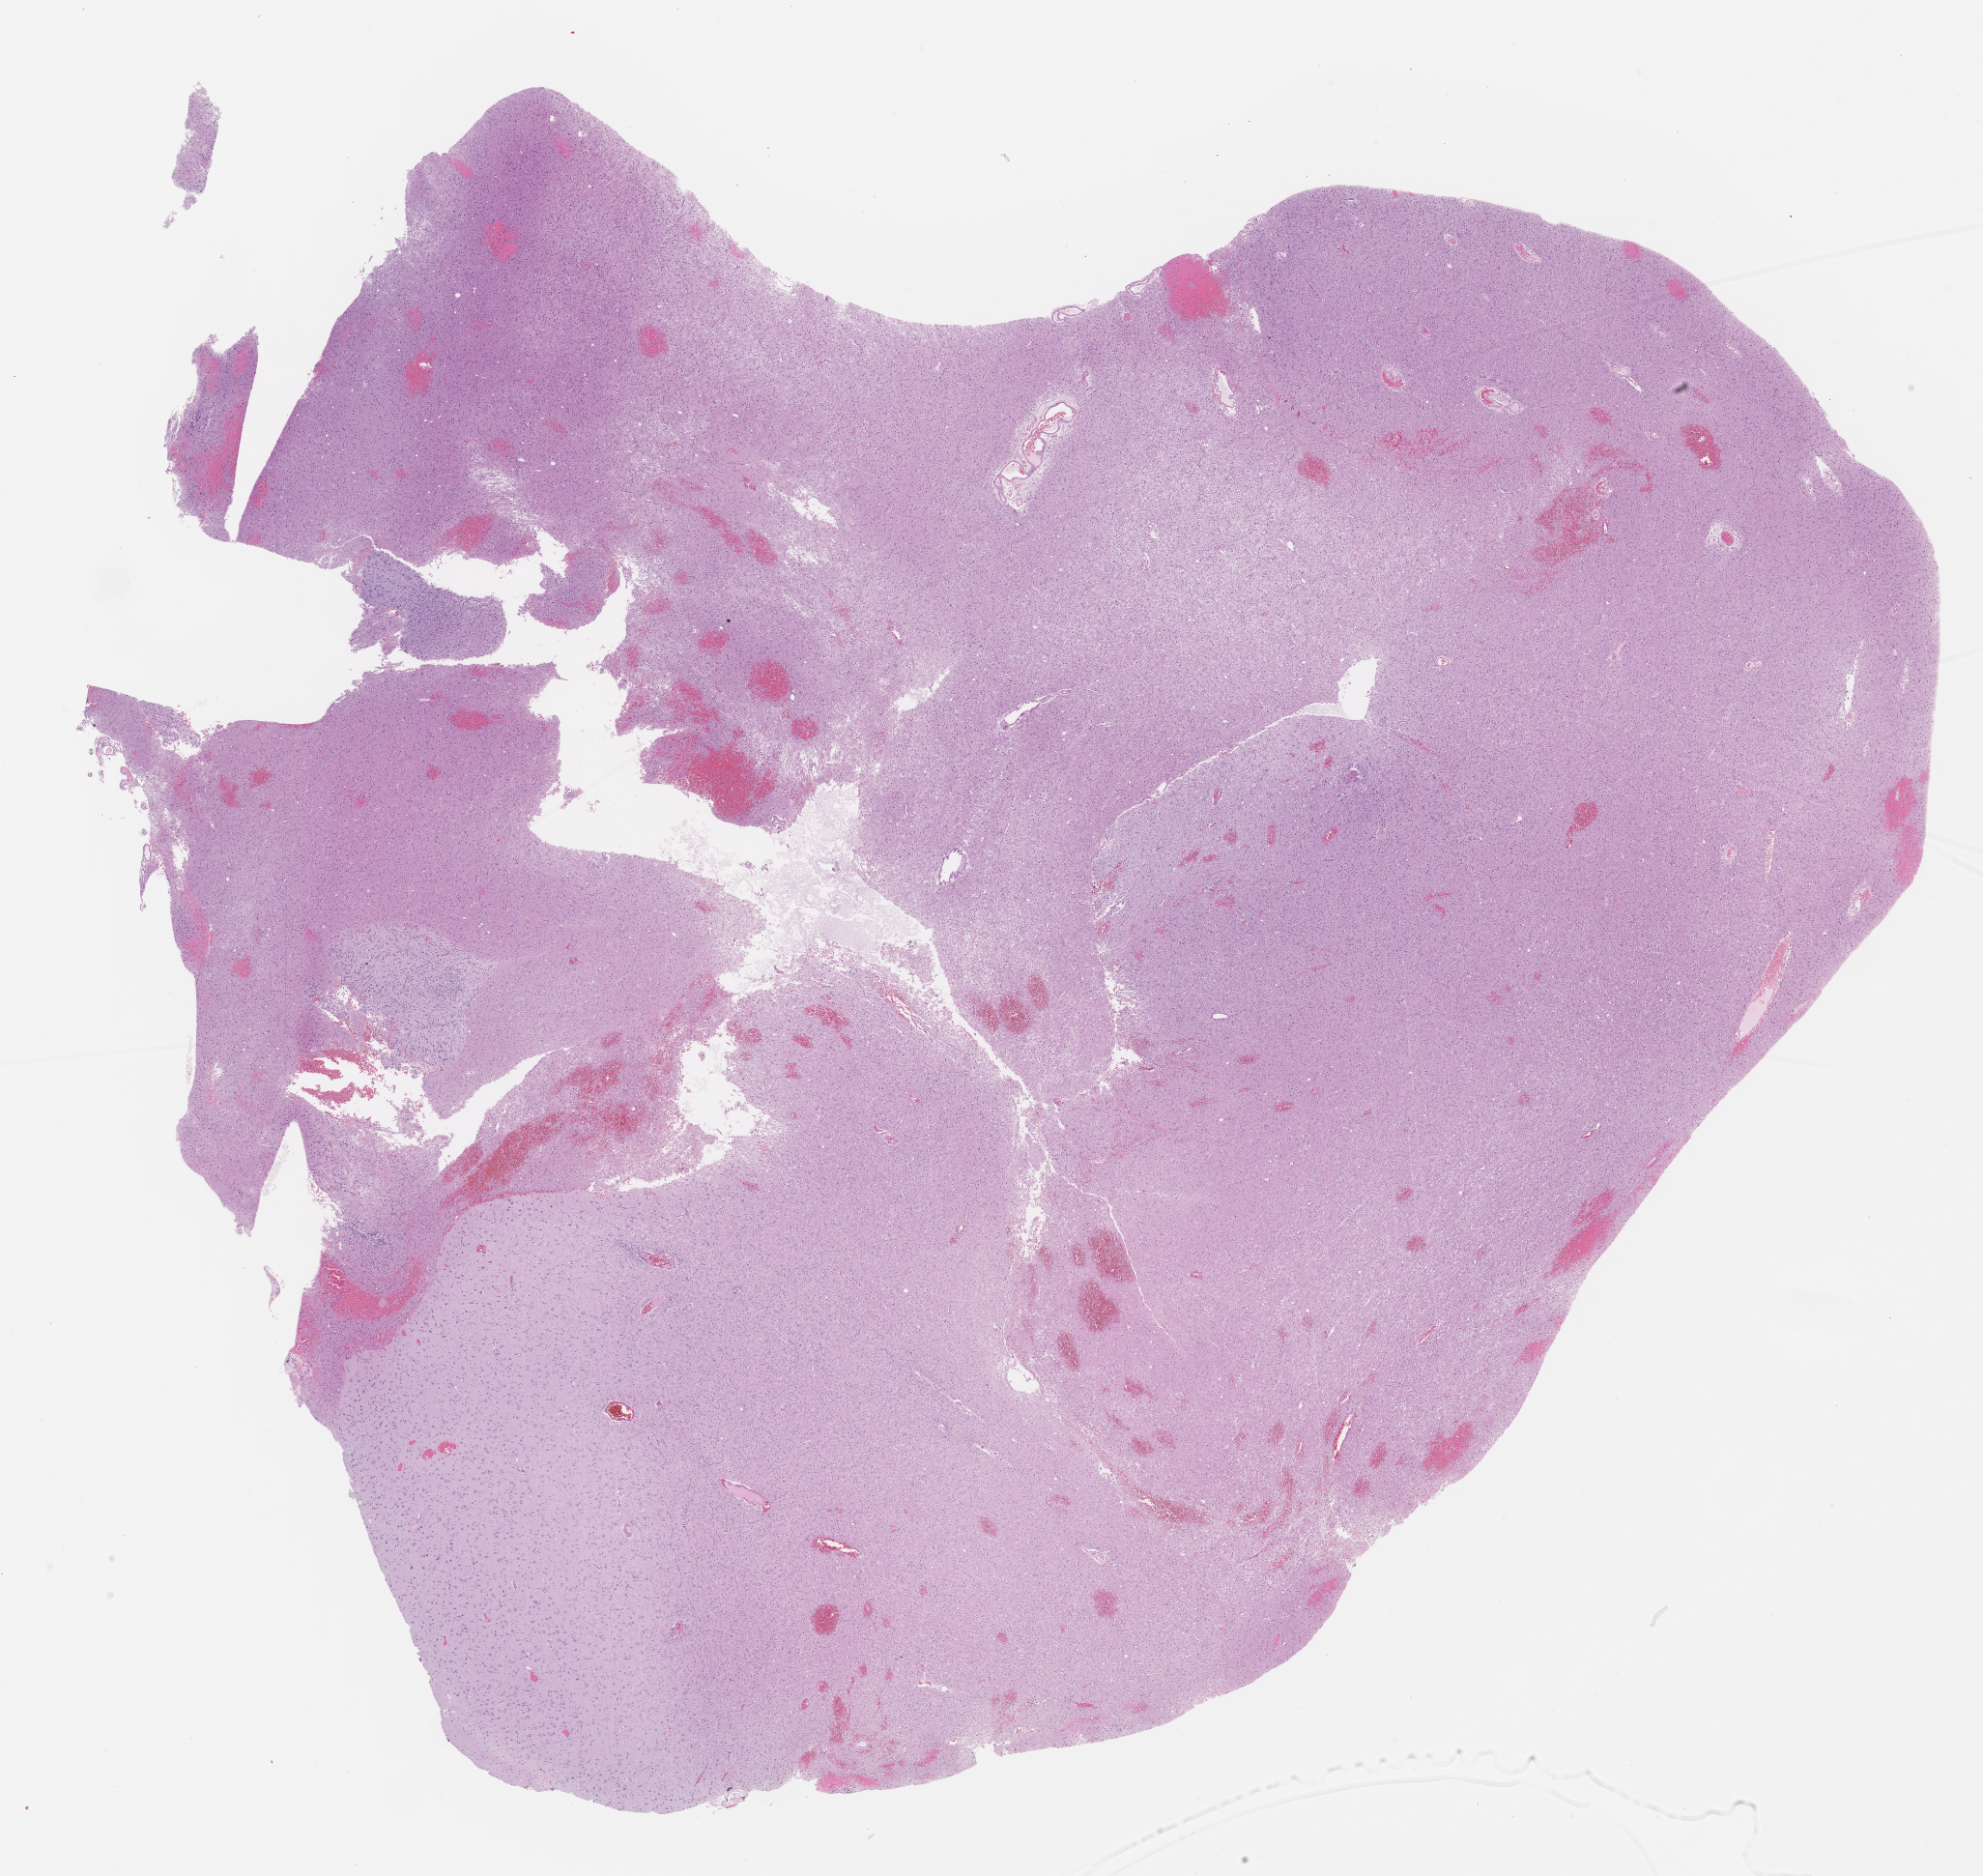
Whole-slide histology image, H&E-stained — shown as a low-resolution overview of the whole scanned area (about 16.5 x 15.6 mm, acquisition: 40x scan), FFPE section, brain, primary tumour sample. Female, age 53 years at initial diagnosis.
Histologic diagnosis: Oligodendroglioma, NOS.